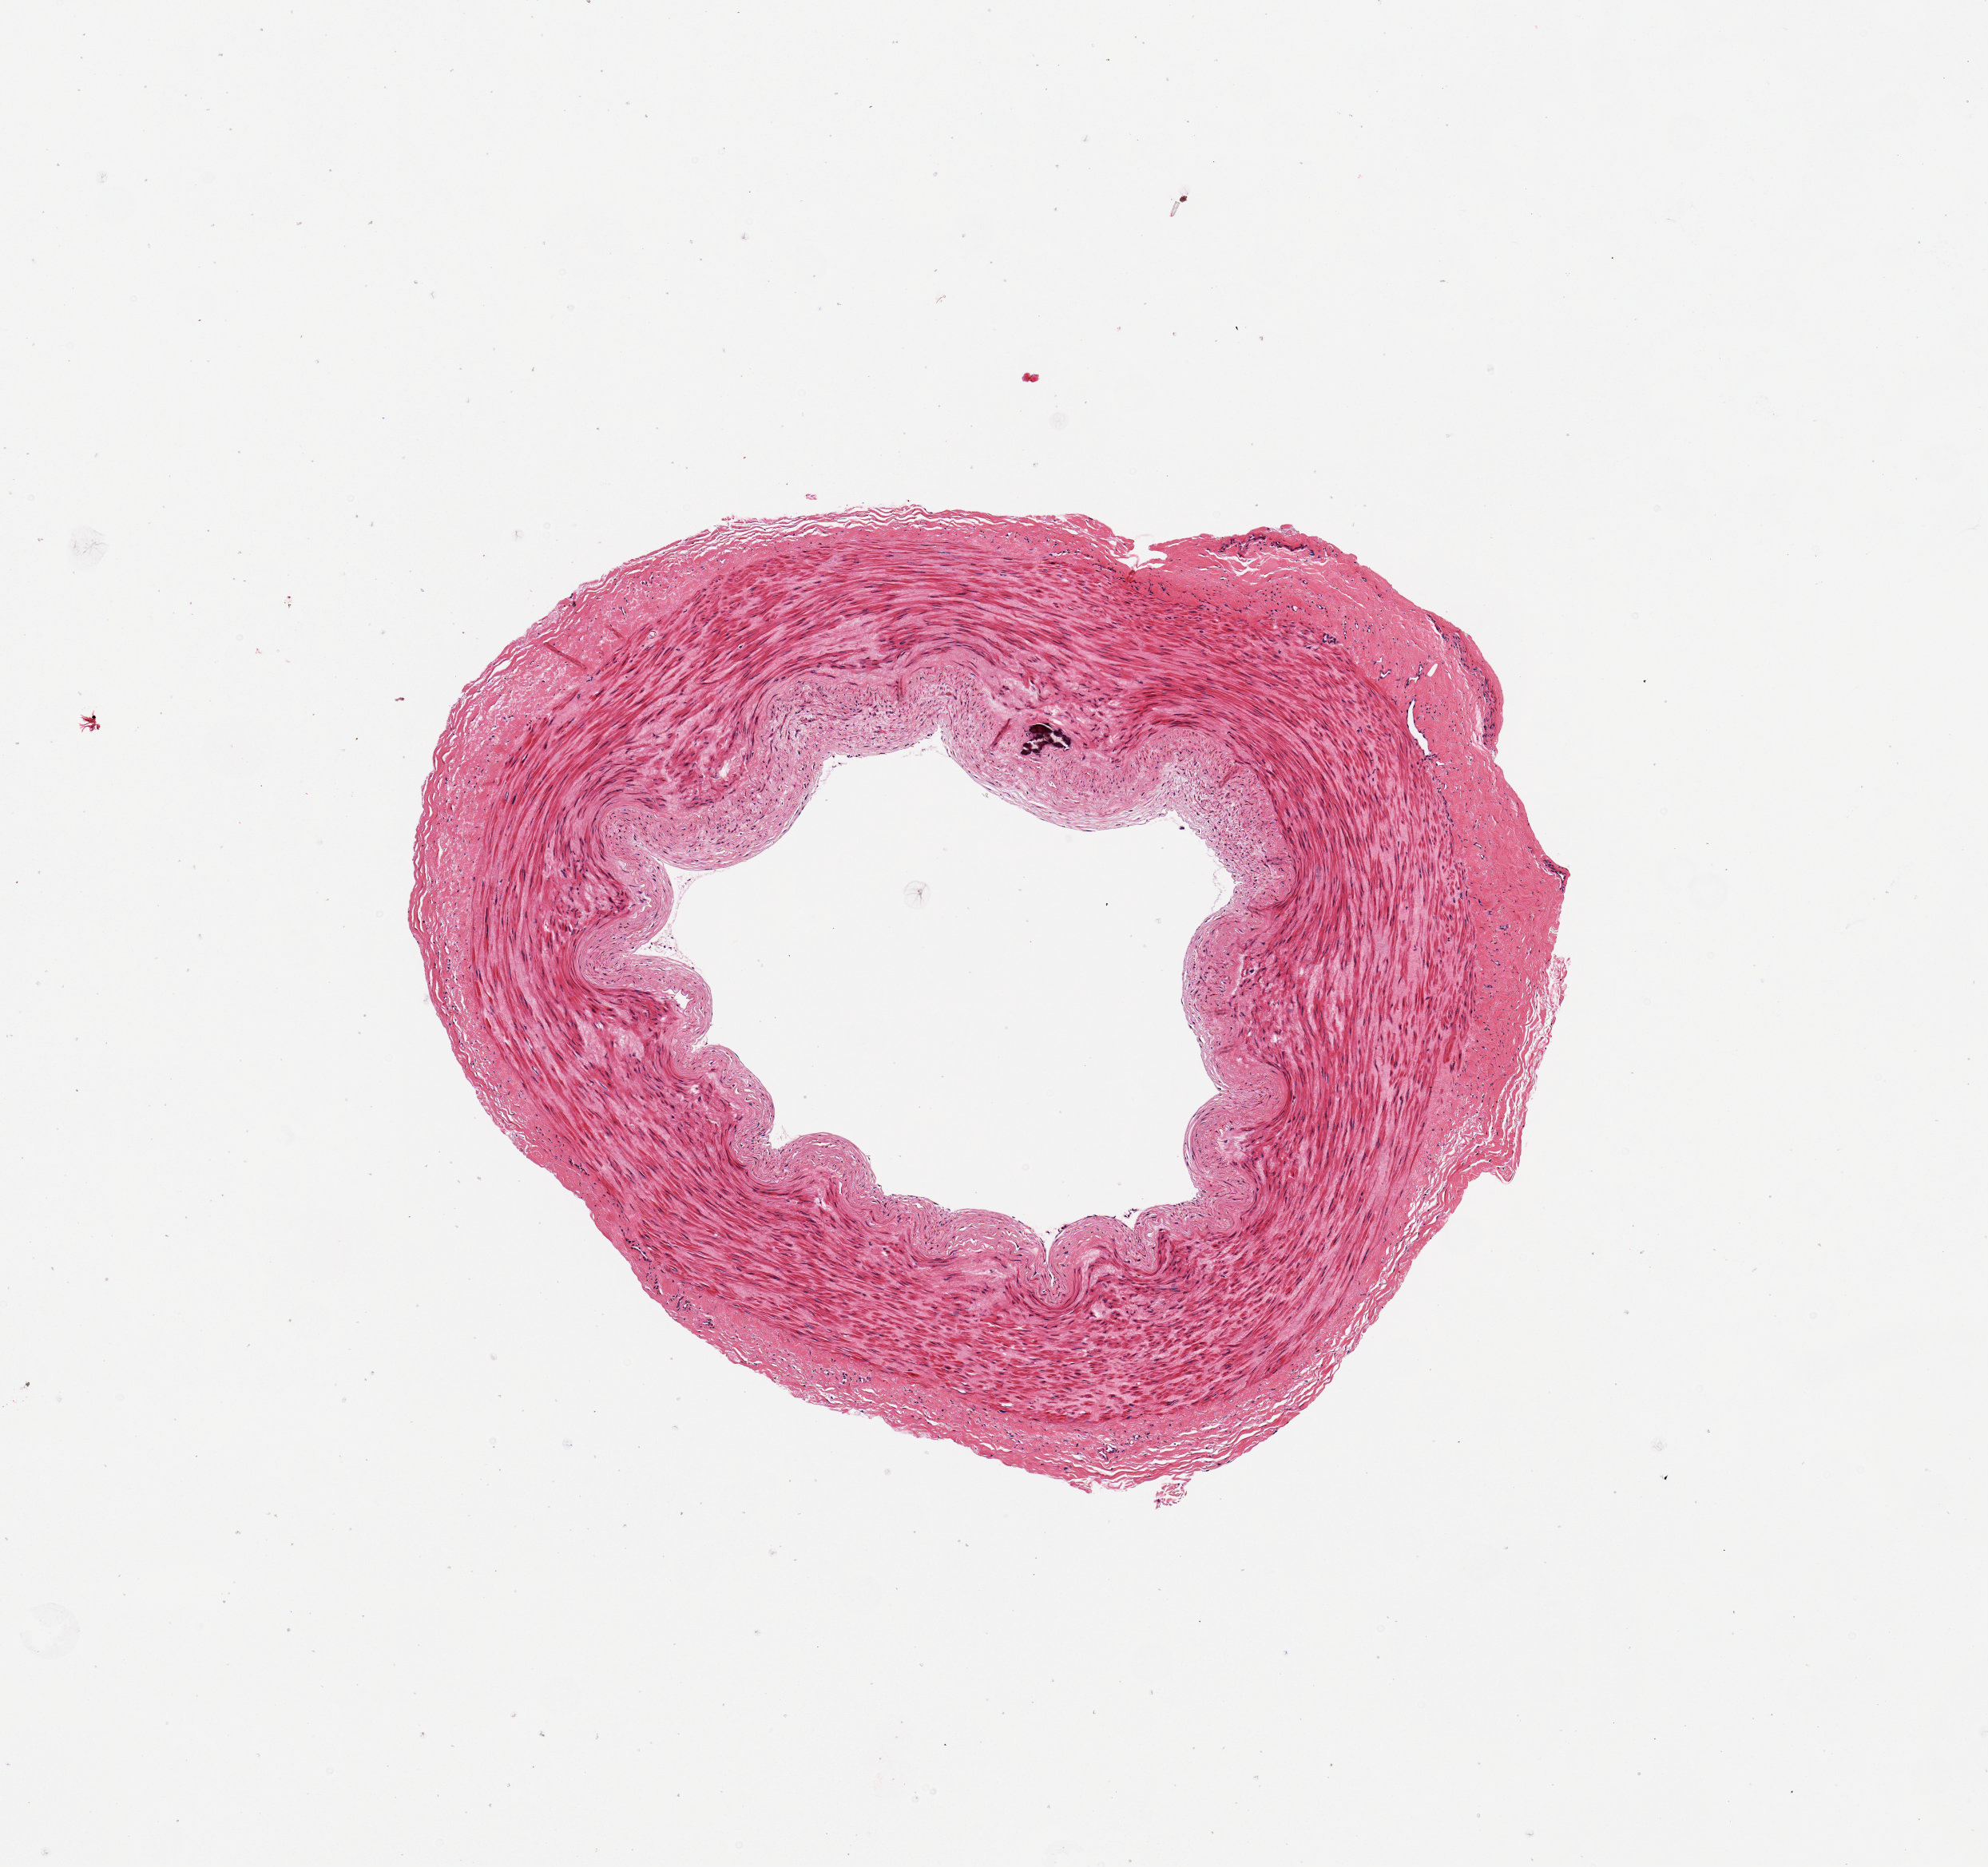
Whole-slide image, hematoxylin and eosin (H&E) stain — a low-resolution overview of the entire scanned area, about 4.9 x 4.6 mm (acquisition: 20x scan). PAXgene-fixed, paraffin-embedded tissue. Target tissue: tibial artery. Donor tissue sample. Donor: male.
• review note (as recorded): Peripheral nerve, not artery. Nerve accounts for central 50% of specimen; remainder is fat. Verified mix-up.VAI to change site from Artery to Nerve